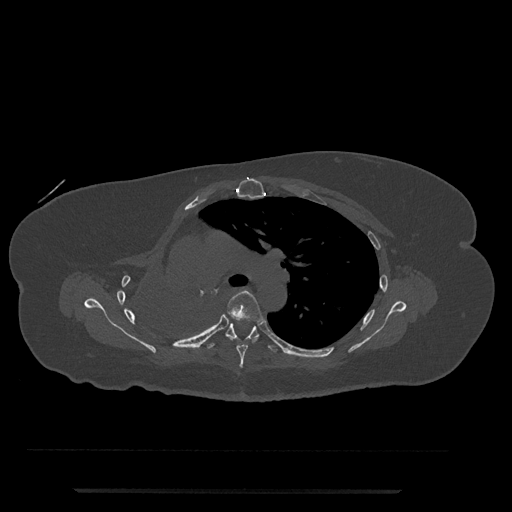
CT including the spine, one axial slice. Position 521 of 797 along the scan axis. Reconstruction kernel Br40s/3. 120 kVp. Bone window (W 1800 / L 400 HU). 0.5 mm slice thickness. 512 × 512 image matrix. Patient: female, 51 years. Case-level facts recorded for this patient, not image findings: primary cancer: neuro; vertebrae with lytic lesions (as recorded): T8.
Annotated regions visible in this slice (semi-automatically segmented with operator editing):
- T5 vertebra: bounding box (x1, y1, x2, y2) in pixels: (225, 290, 263, 368)
- T6 vertebra: (207, 323, 277, 352)